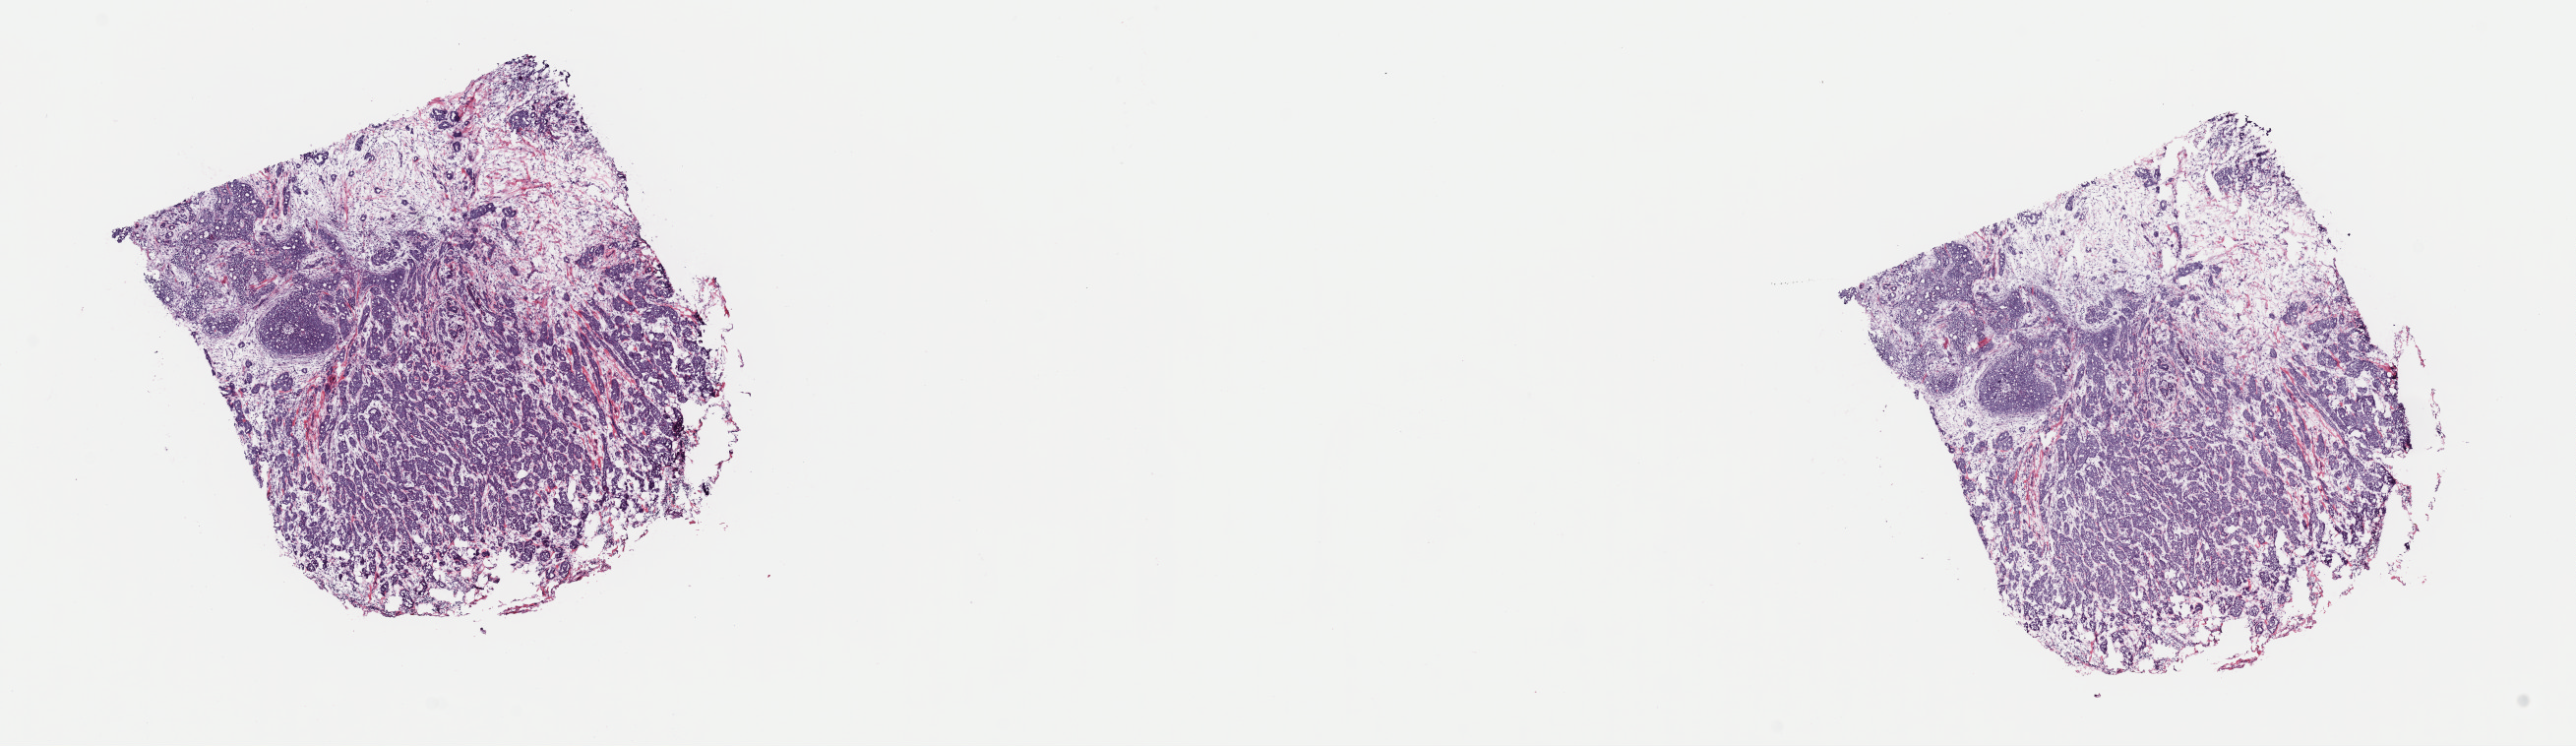
Whole-slide histology image, H&E, shown as a low-resolution overview of the whole scanned area (about 20.7 x 6.0 mm, from a 40x scan), frozen section from the top of the tissue portion, sample: primary tumour, breast. Patient: female, age at initial diagnosis 43 years. Slide review estimates, as recorded: tumour cells 70%, tumour nuclei 70%, normal cells 12%, stromal cells 16%, necrosis 2%. Inflammatory infiltration, as recorded: lymphocyte infiltration 5%, monocyte infiltration 1%, neutrophil infiltration 1%.
* histologic diagnosis: Infiltrating duct carcinoma, NOS
* AJCC pathologic stage: IIB (7th edition)
* laterality: right